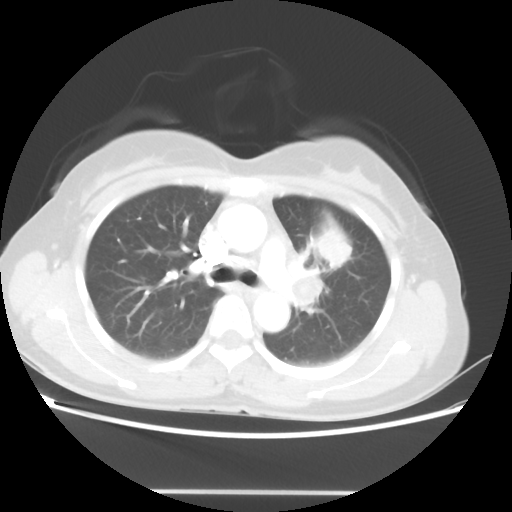
Chest CT, one axial slice; position 30 of 46 along the scan axis; reconstruction kernel STANDARD; 100 kVp; lung window (W 1500 / L -600 HU); 512 × 512 image matrix. Female patient, age 50 years. Case-level facts recorded for this patient, not image findings: clinical TNM (as recorded): T1c N1 M0; histopathological grade: G3.
Annotated regions visible in this slice (bounding box drawn by a radiologist):
- lung tumour (recorded histology: adenocarcinoma): bounding box [x1, y1, x2, y2] px = [317, 226, 352, 267]